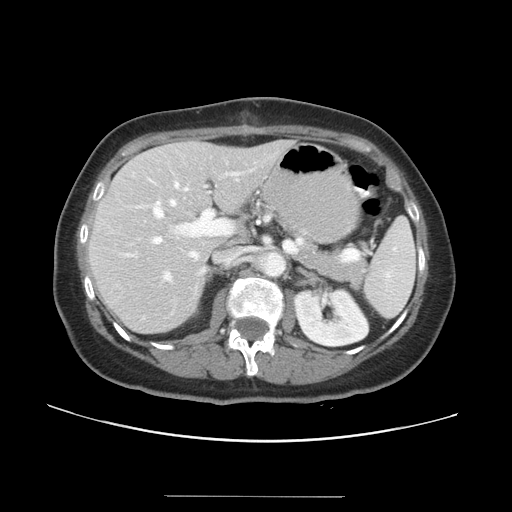
Contrast-enhanced abdominal CT, one axial slice. Slice 20 of 34 in the series (ordered by position). Reconstruction kernel STANDARD. 120 kVp. Intravenous contrast given. Soft-tissue window (W 400 / L 40 HU). 5 mm slice thickness. 512 × 512 image matrix, field of view 382 × 382 mm. Female patient, age 69 years. Case-level facts recorded for this patient, not image findings: diagnosis: colorectal cancer liver metastases, imaged before liver resection; multiple liver metastases: yes; largest metastasis: 1.4 cm.
Structures marked on this image (expert manual segmentation):
- hepatic veins: box from (x=163, y=172) to (x=238, y=282) px
- liver: (x=90, y=140)–(x=293, y=333)
- planned liver remnant (the part of the liver to remain after resection): (x=90, y=140)–(x=293, y=333)
- portal vein (with intrahepatic branches): (x=124, y=173)–(x=359, y=261)